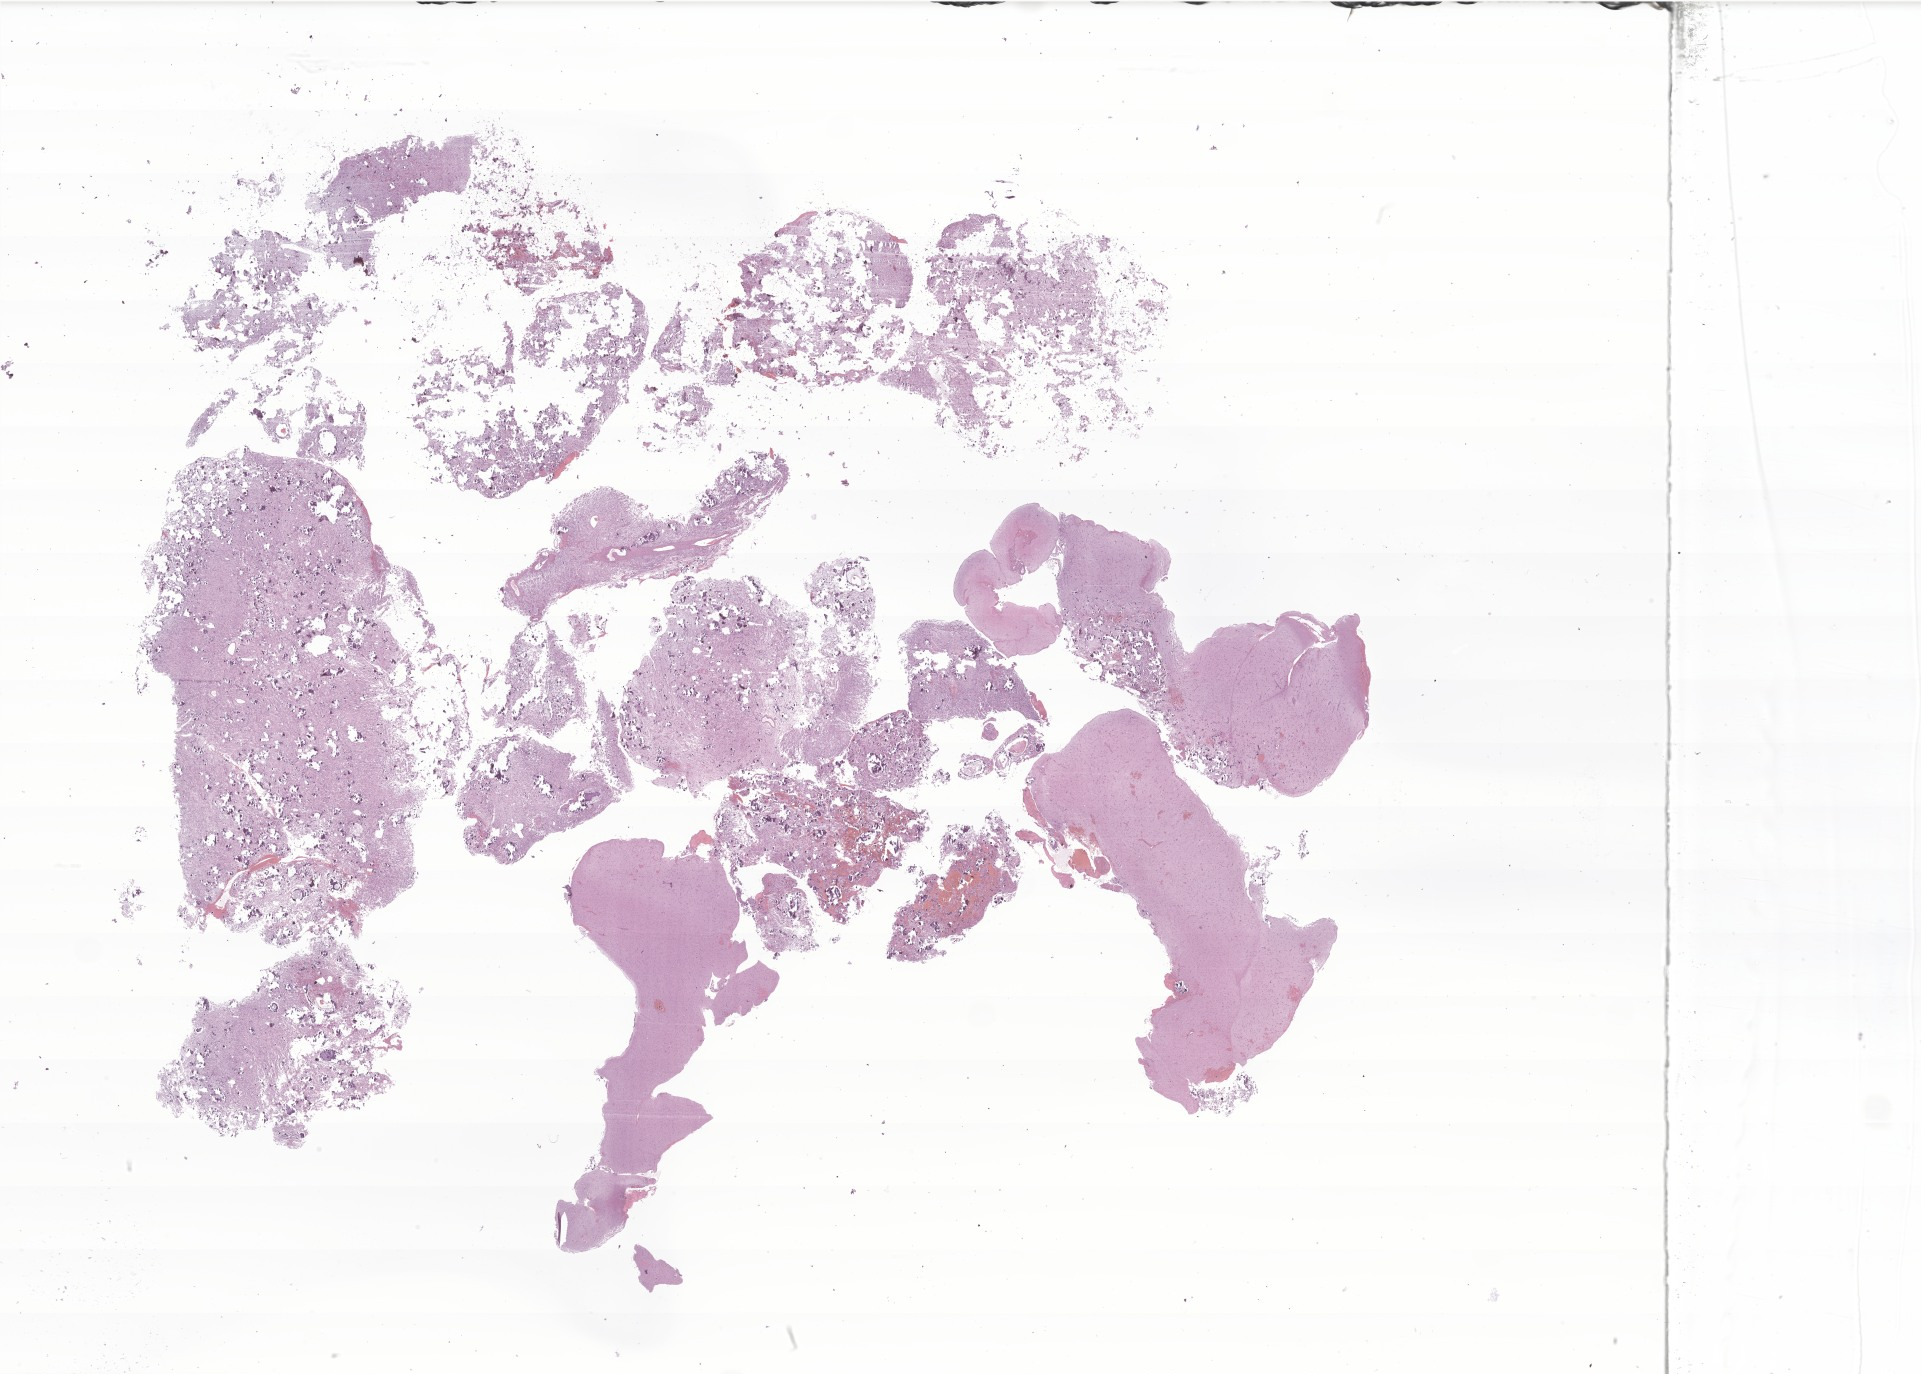
H&E whole-slide image of tumor tissue from the temporal lobe, low-resolution overview of the scanned area, about 32.4 x 23.2 mm; formalin-fixed, paraffin-embedded (FFPE) tissue. Patient female; age 185 months (15 years 5 months).
* recorded diagnosis: Glioma, malignant